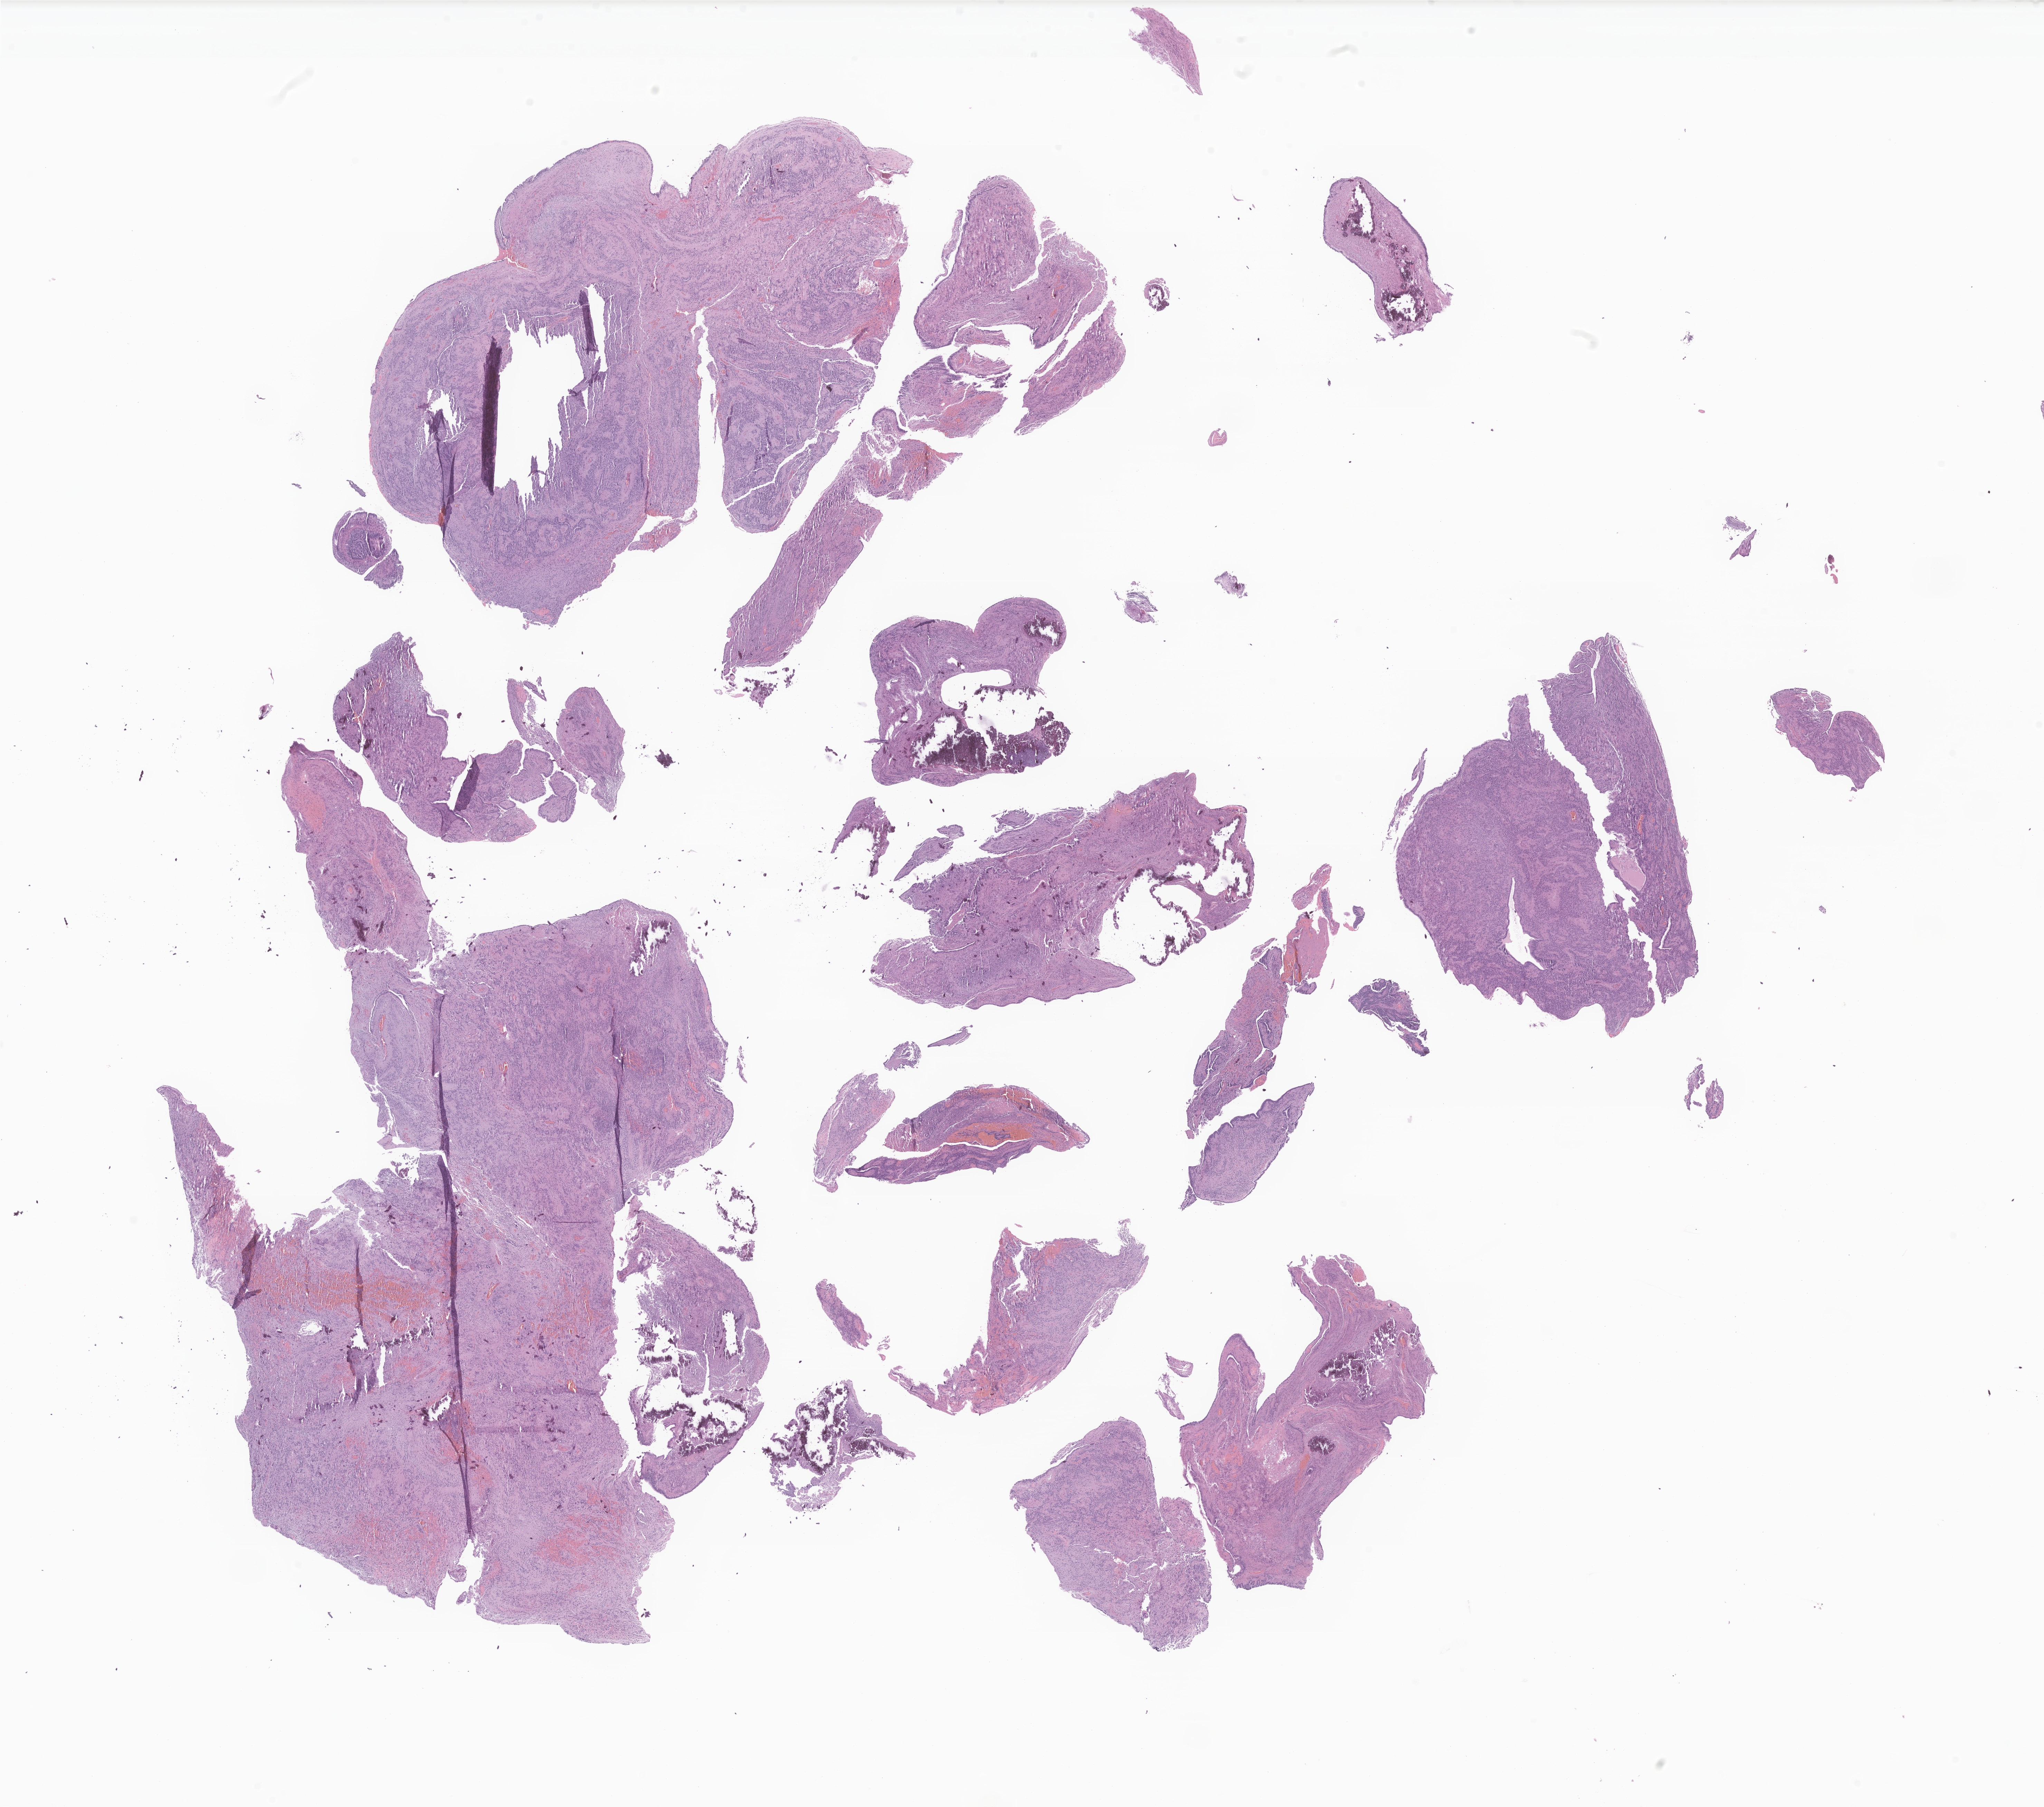
H&E whole-slide image of tumor tissue from the brain — shown as a low-resolution overview of the whole scanned area (about 24.9 x 22.1 mm). Formalin-fixed paraffin-embedded section. Female patient, age 118 months (9 years 10 months).
Diagnosis (ICD-O-3 morphology term): Ependymoma, NOS.